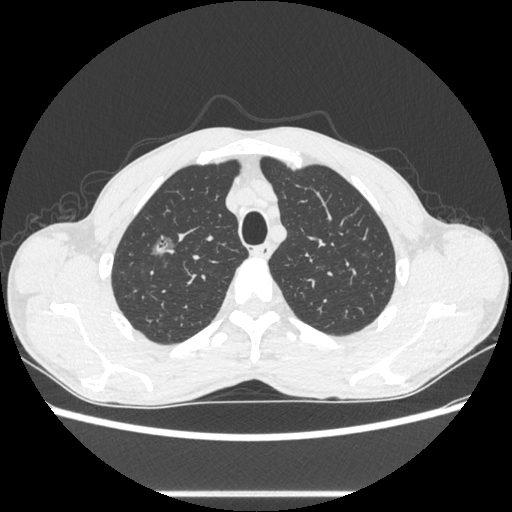
Chest CT, one axial slice. Position 483 of 600 along the scan axis. Lung window (W 1500 / L -600 HU). 0.62 mm slice thickness. 512 × 512 image matrix, field of view 357 × 357 mm. Patient: male, 54 years. From the clinical record (not read from this slice): clinical TNM (as recorded): T1a N0 M0.
Annotated regions visible in this slice (rectangle marked by the reading radiologist):
- lung tumour (recorded histology: adenocarcinoma): bounding box [x1, y1, x2, y2] px = [144, 231, 180, 266]